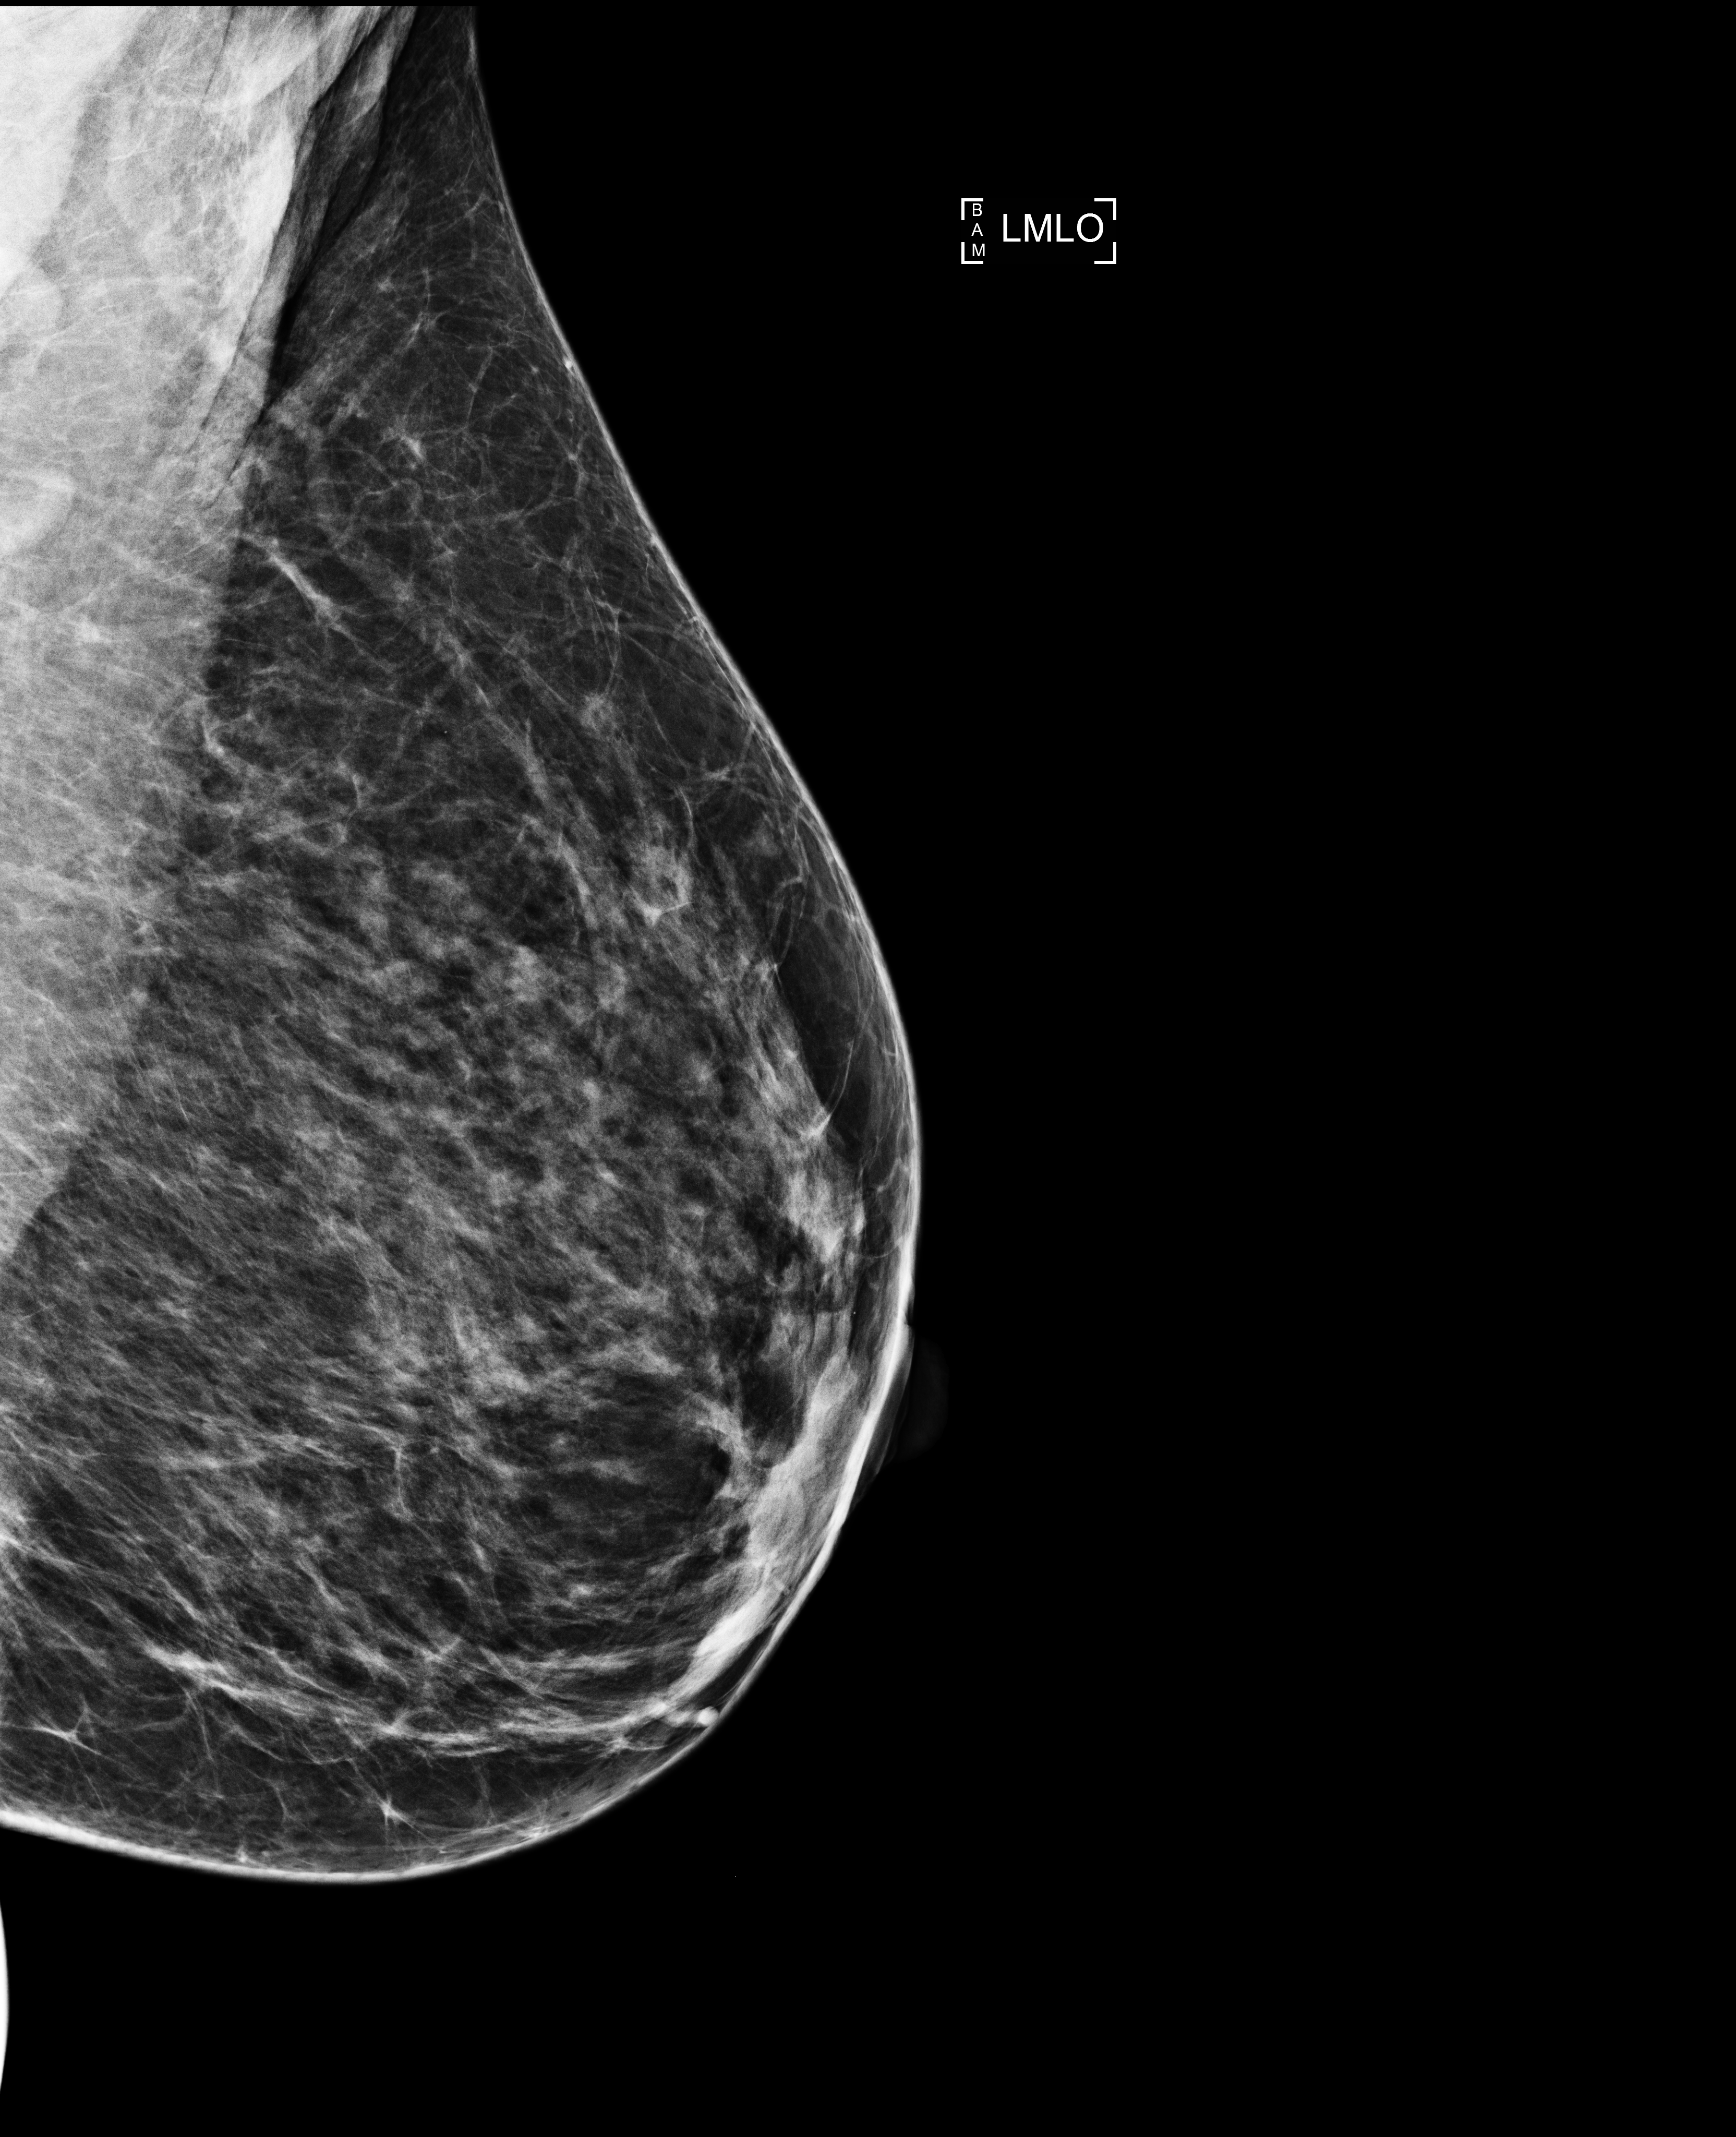
Annual screening mammography examination, compressed breast thickness 62 mm, system: Selenia Dimensions. Female patient, age 44 years.
Image type: full-field digital mammogram. Breast: left. Projection: MLO view.